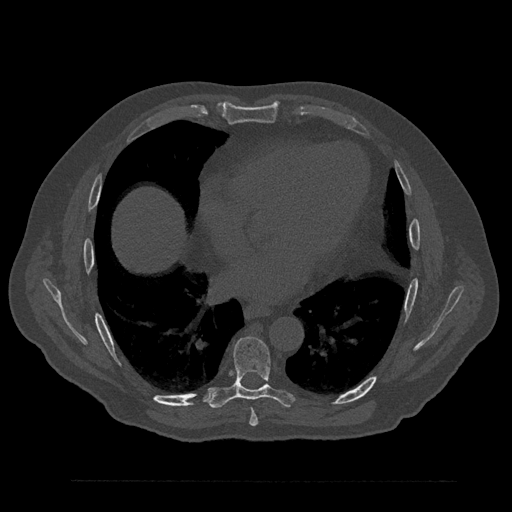
CT including the spine, one axial slice; slice 461 of 797 in the series (ordered by position); 120 kVp; bone window (W 1800 / L 400 HU); 512 × 512 image matrix, field of view 430 × 430 mm. Male patient, age 61 years. From the clinical record (not read from this slice): primary cancer: prostate.
Structures marked on this image (semi-automatically segmented with operator editing):
- T7 vertebra: bounding box [x1, y1, x2, y2] px = [249, 408, 258, 426]
- T8 vertebra: [208, 336, 294, 409]